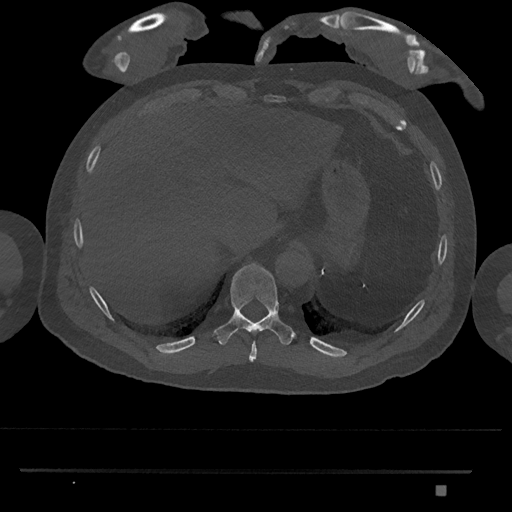
CT including the spine, one axial slice; slice 1006 of 1134 in the series (ordered by position); reconstruction kernel Br40s/3; 120 kVp; bone window (W 1800 / L 400 HU); 0.5 mm slice thickness; 512 × 512 image matrix, field of view 429 × 429 mm. Patient: male, 65 years. Case-level facts recorded for this patient, not image findings: primary cancer: prostate.
Outlined on this slice (semi-automatically segmented with operator editing):
- T10 vertebra: bounding box [x1, y1, x2, y2] px = [214, 263, 295, 345]
- T9 vertebra: [248, 341, 257, 362]